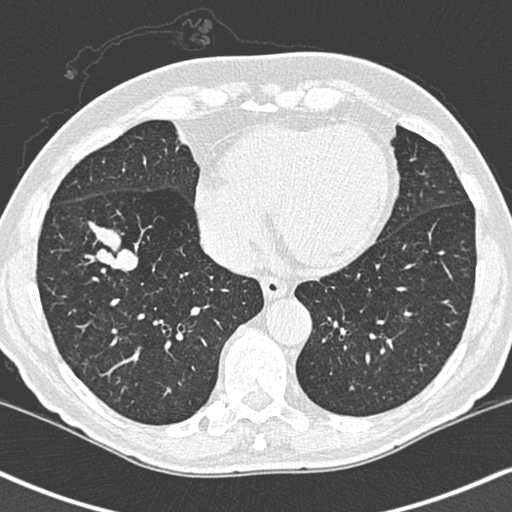
Low-dose screening chest CT, one axial slice. Slice 91 of 248 in the series (ordered by position). 120 kVp. Lung window (W 1500 / L -600 HU). 1.3 mm slice thickness. 512 × 512 image matrix, field of view 323 × 323 mm.
Annotated regions visible in this slice (expert manual segmentation):
- lesion 1 (tumor, lower lobe of right lung): bounding box (x1, y1, x2, y2) in pixels: (88, 183, 138, 234)